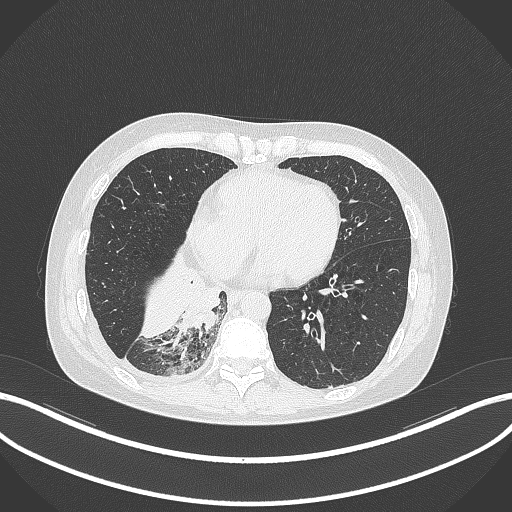
Chest CT, one axial slice; slice 103 of 329 in the series (ordered by position); reconstruction kernel B70f; lung window (W 1500 / L -600 HU); 1 mm slice thickness; 512 × 512 image matrix, field of view 400 × 400 mm. Female patient, age 63 years. Case-level facts recorded for this patient, not image findings: clinical TNM (as recorded): T1c N0 M0.
Outlined on this slice (bounding box drawn by a radiologist):
- lung tumour (recorded histology: adenocarcinoma): bounding box <183,278,223,332> (left, top, right, bottom; pixels)